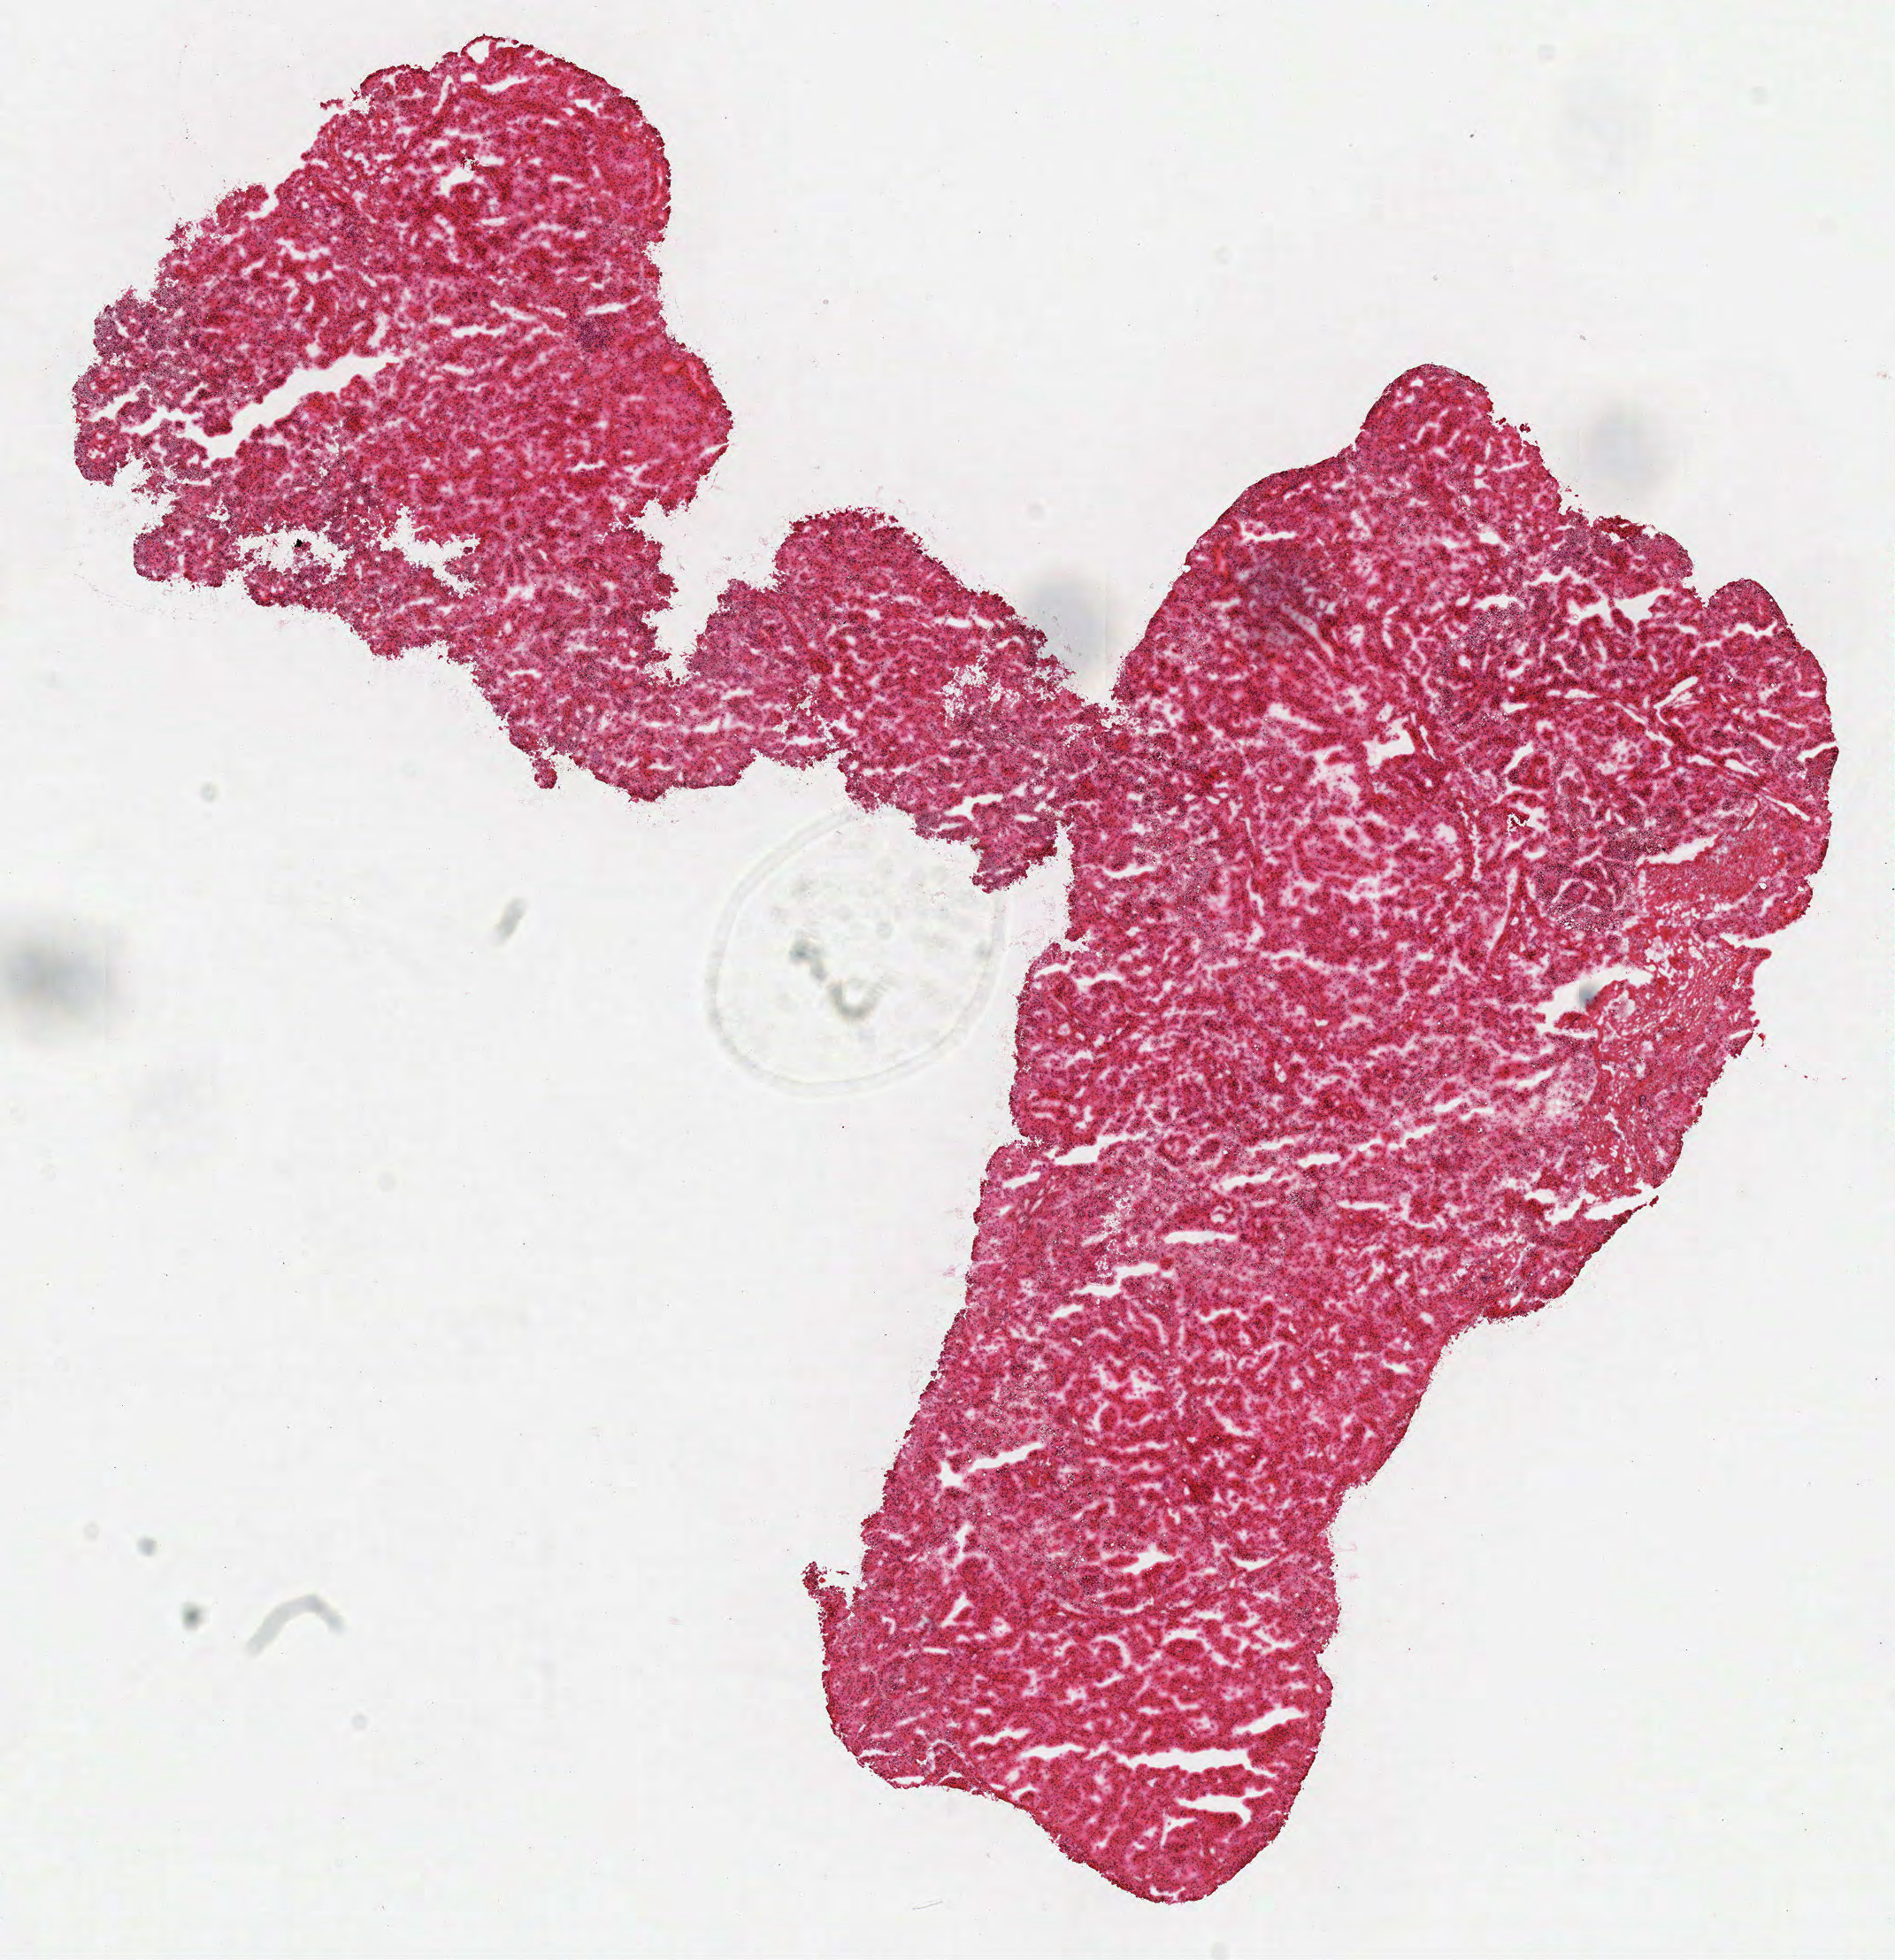
Whole-slide histology image, H&E-stained — shown as a low-resolution overview of the whole scanned area (about 8.4 x 8.7 mm); frozen section from the top of the tissue portion; sample: primary tumour, kidney. Male patient; age at initial diagnosis 75 years. Slide review estimates, as recorded: tumour cells 95%, tumour nuclei 80%, normal cells 0%, stromal cells 5%, necrosis 0%.
AJCC pathologic stage: I. Diagnosis: Papillary adenocarcinoma, NOS.